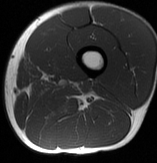
MRI of an extremity soft-tissue mass, one axial slice; position 15 of 70 along the scan axis; MR volume resampled by the dataset authors to the PET/CT grid (not the native acquisition matrix); 3.27 mm slice thickness; 157 × 163 image matrix, field of view 153 × 159 mm. Male patient. From the clinical record (not read from this slice): histological type: extraskeletal osteosarcoma; grade: high; site of the primary tumour: left adductur.
Annotated regions visible in this slice (expert contour drawn on MRI and transferred to this co-registered scan by the dataset authors):
- gross tumour volume (mass): box from (x=74, y=81) to (x=91, y=93) px